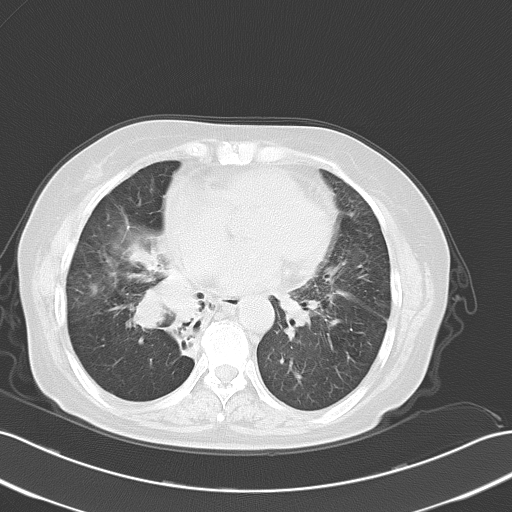
Chest CT, one axial slice; position 30 of 62 along the scan axis; lung window (W 1500 / L -600 HU); 5 mm slice thickness; 512 × 512 image matrix, field of view 353 × 353 mm. Patient: female, 65 years. Case-level facts recorded for this patient, not image findings: clinical TNM (as recorded): T1c N3 M0; histopathological grade: G3.
Structures marked on this image (bounding box drawn by a radiologist):
- lung tumour (recorded histology: small cell carcinoma): box from (x=122, y=268) to (x=198, y=336) px